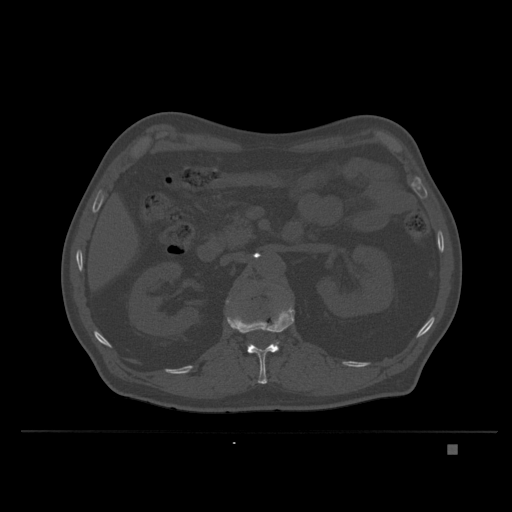
CT including the spine, one axial slice. Slice 133 of 435 in the series (ordered by position). Bone window (W 1800 / L 400 HU). 1.5 mm slice thickness. 512 × 512 image matrix, field of view 434 × 434 mm. Male patient, age 73 years. From the clinical record (not read from this slice): primary cancer: skin.
Outlined on this slice (semi-automatic segmentation, software-assisted and operator-edited):
- L1 vertebra: box from (x=227, y=306) to (x=295, y=384) px